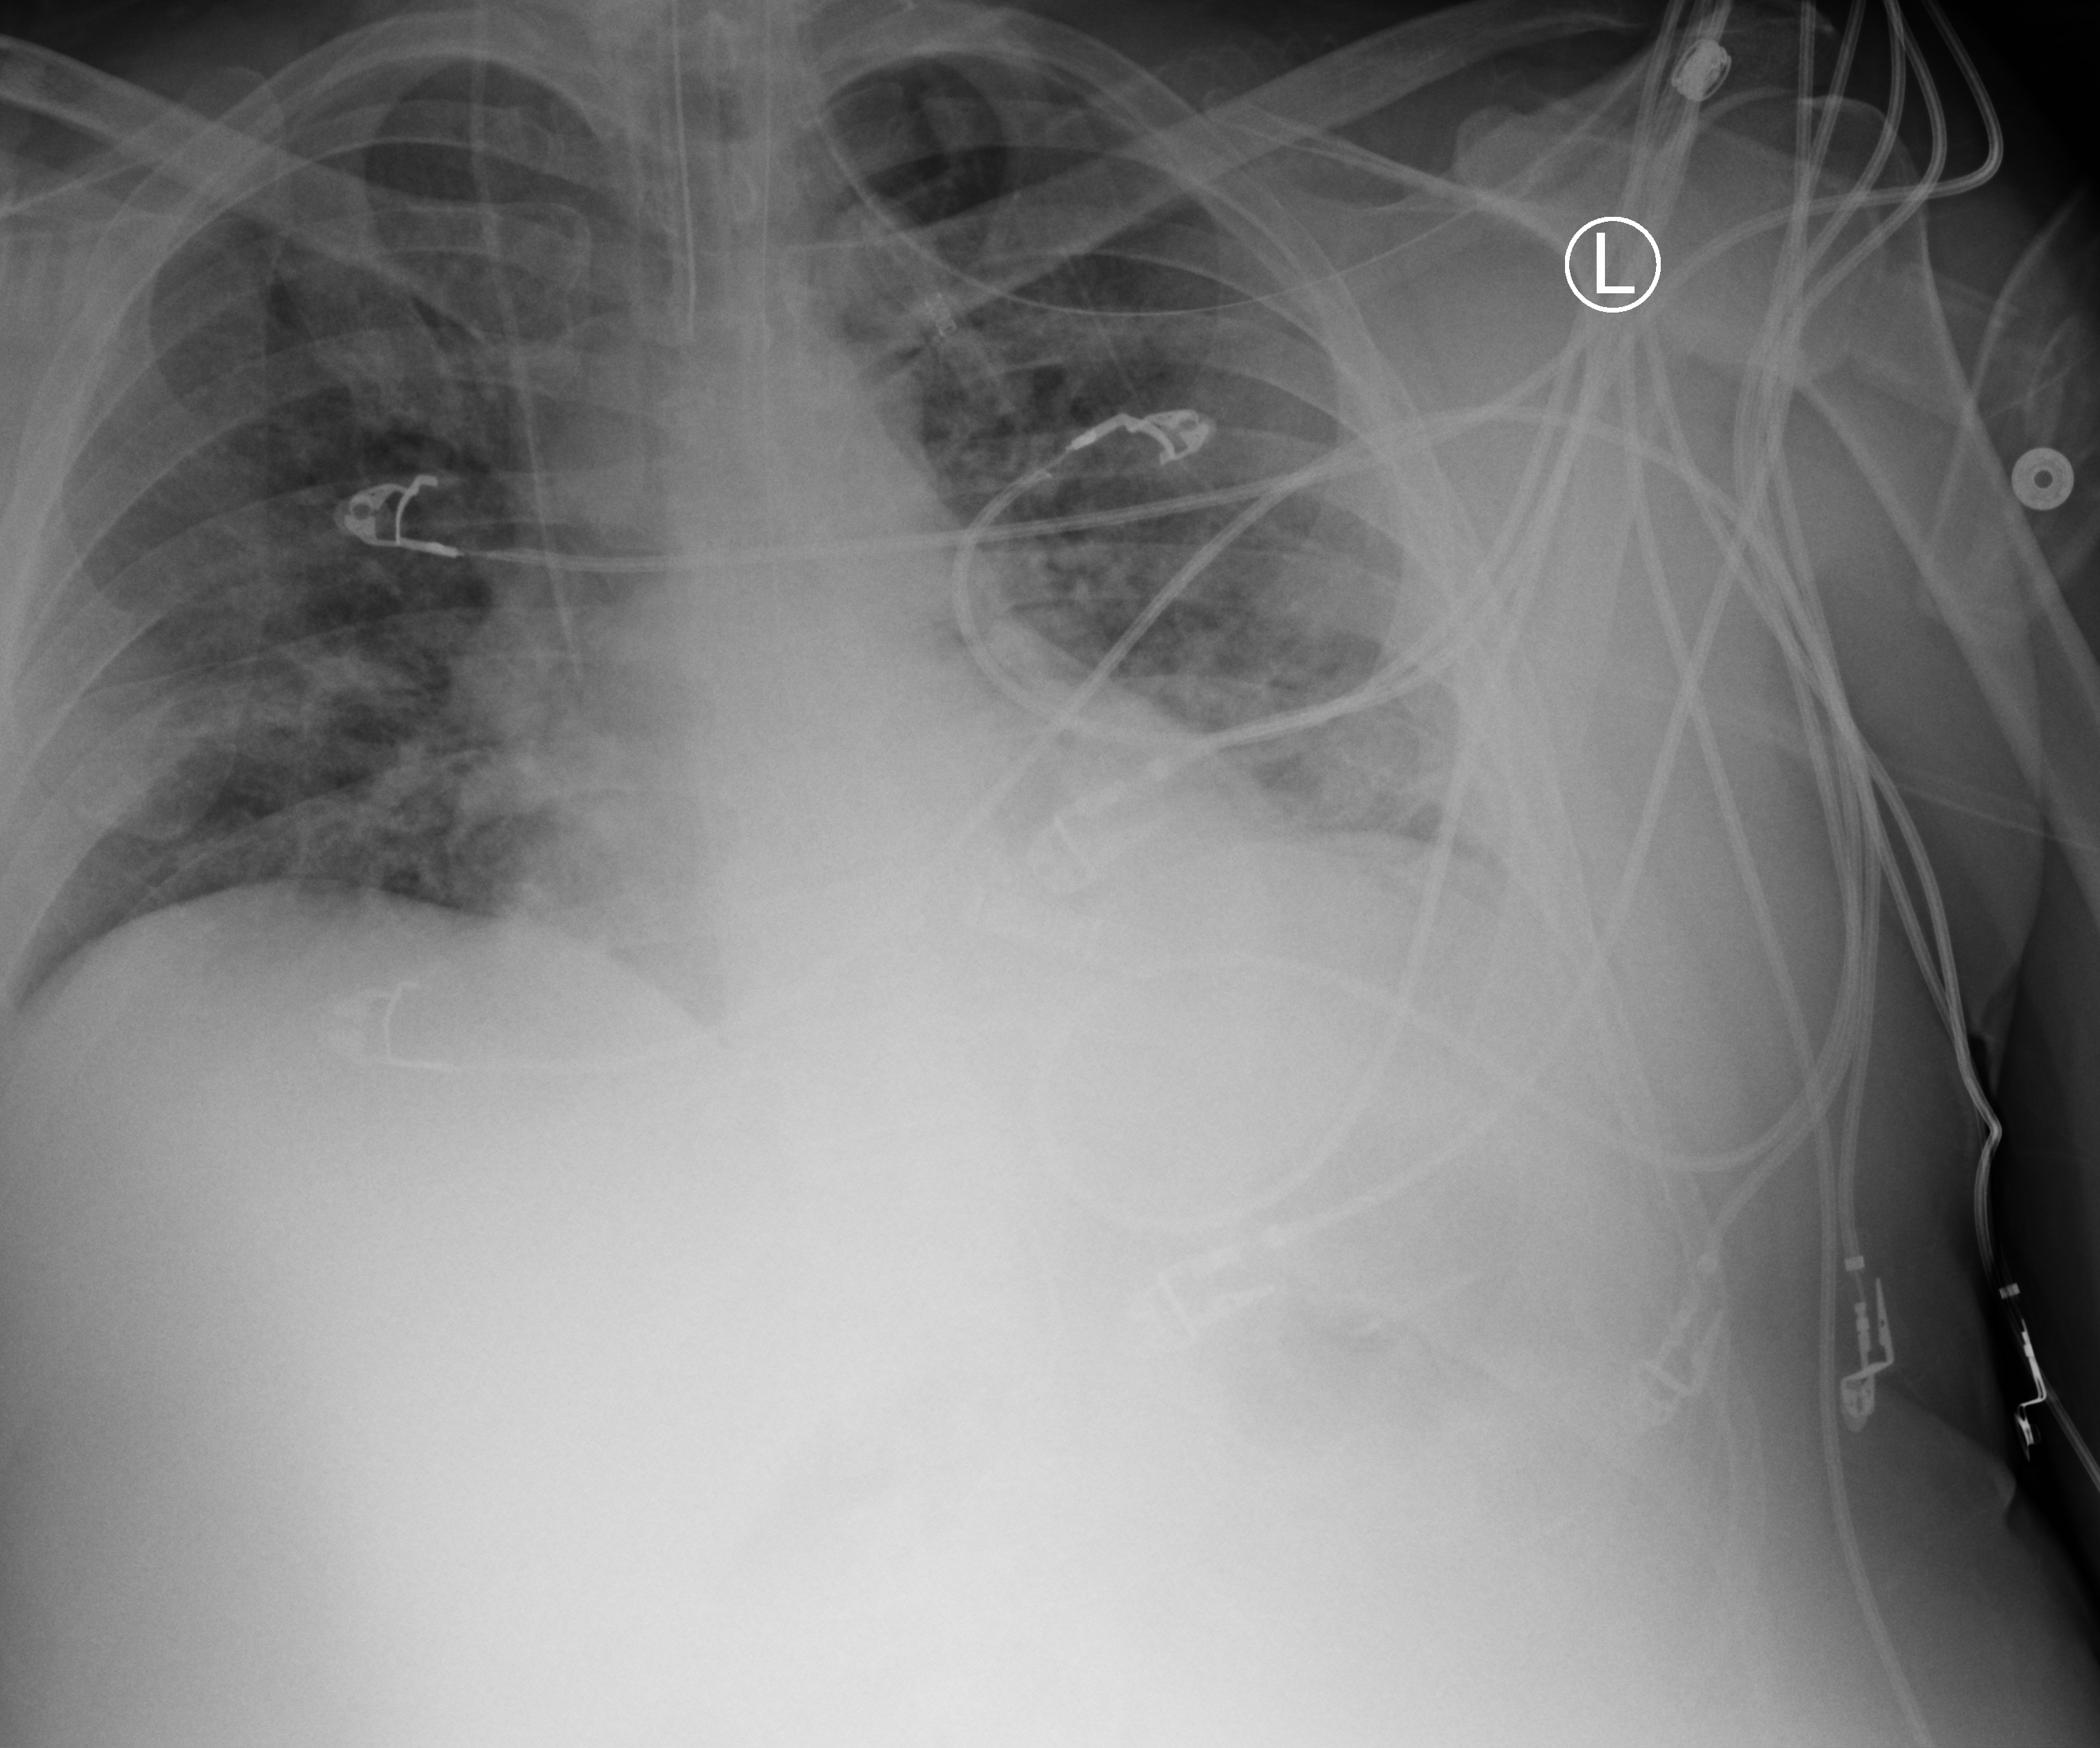
Bedside chest radiograph (computed radiography), anteroposterior (AP) projection. Male patient hospitalised with COVID-19, age 18–59 years.
Hospital-stay facts (about this admission, not read from this image; timing relative to this image not recorded):
- hypertension (admission record): yes
- mechanically ventilated during this hospital stay: yes
- admitted to intensive care during this hospital stay: yes